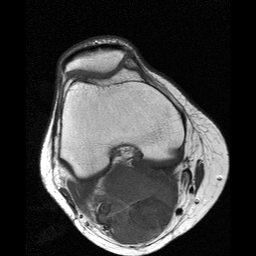
MRI of an extremity soft-tissue mass, one axial slice. Position 11 of 25 along the scan axis. 256 × 256 image matrix, field of view 160 × 160 mm. Female patient. Case-level facts recorded for this patient, not image findings: histological type: liposarcoma; site of the primary tumour: right thigh.
Annotated regions visible in this slice (expert manual segmentation):
- gross tumour volume (mass): bounding box [x1, y1, x2, y2] px = [89, 162, 179, 246]